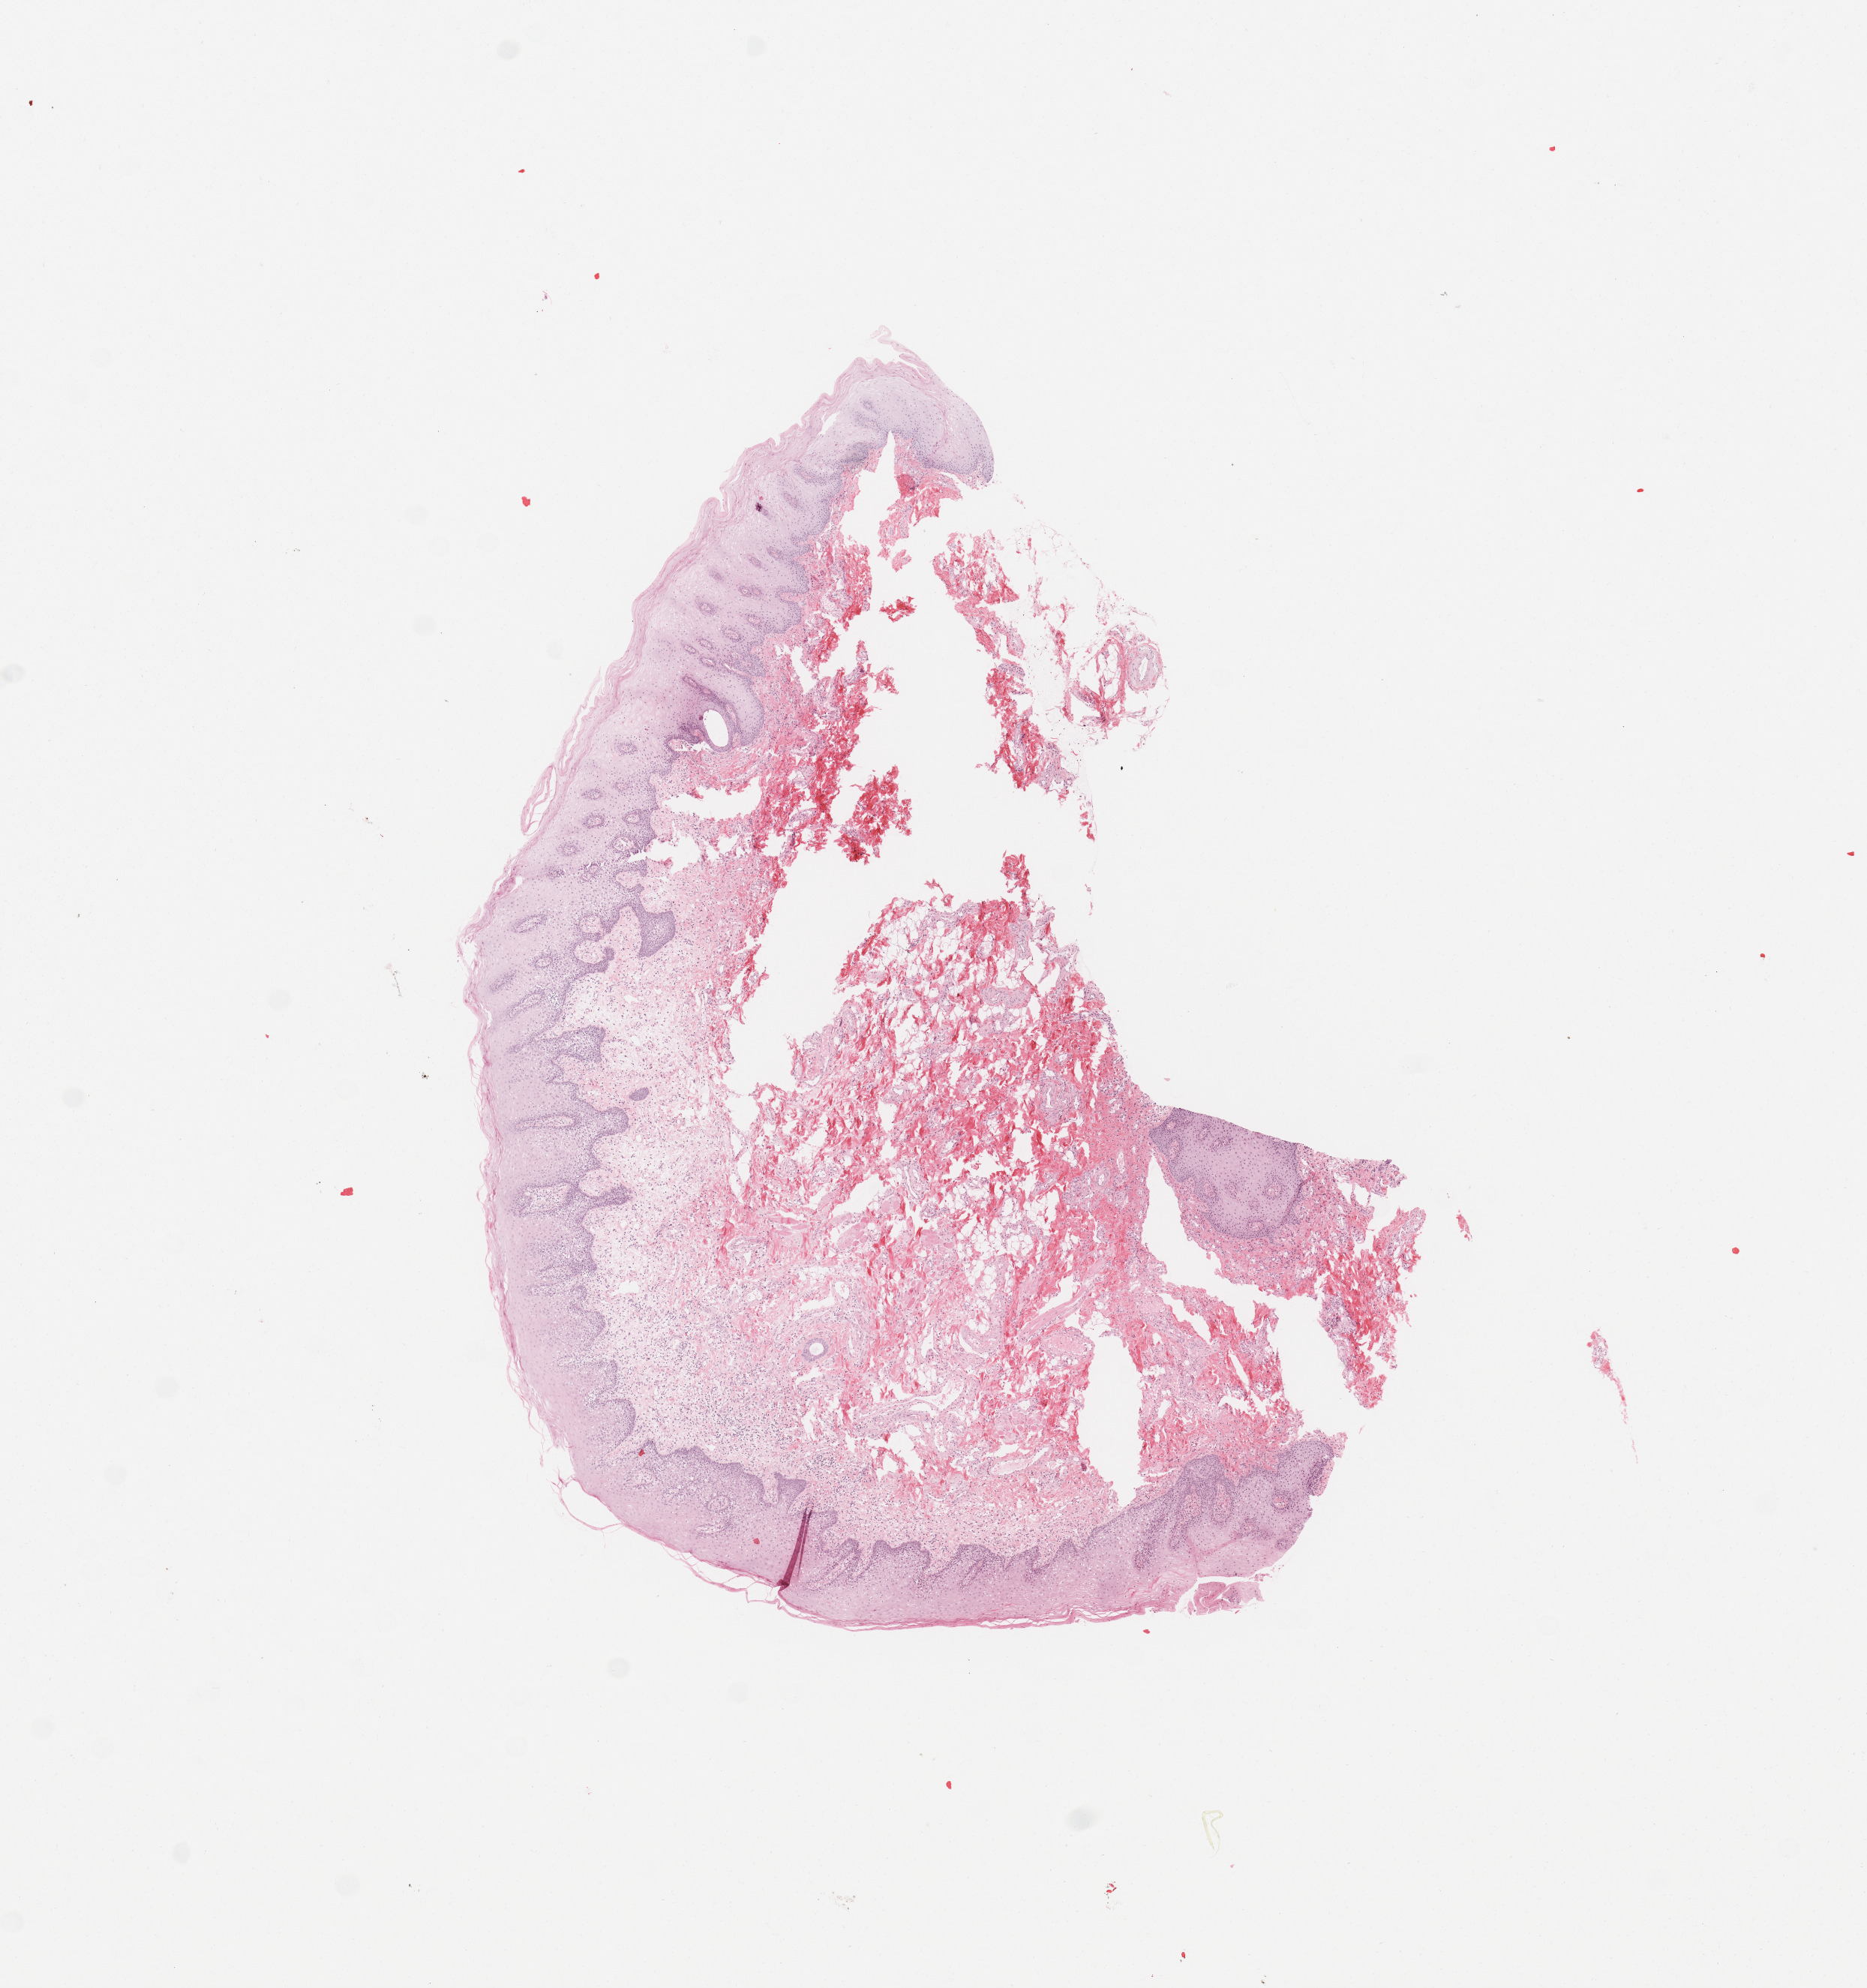
Whole-slide histology image, H&E-stained, low-resolution overview of the scanned area, about 9.8 x 10.5 mm (acquisition: 20x scan); normal (non-tumour) tissue sample, sampled site: lip. 54-year-old male patient.
* this section: normal (non-tumour) tissue from the same patient
* patient diagnosis: Squamous cell carcinoma, NOS (lip, NOS)